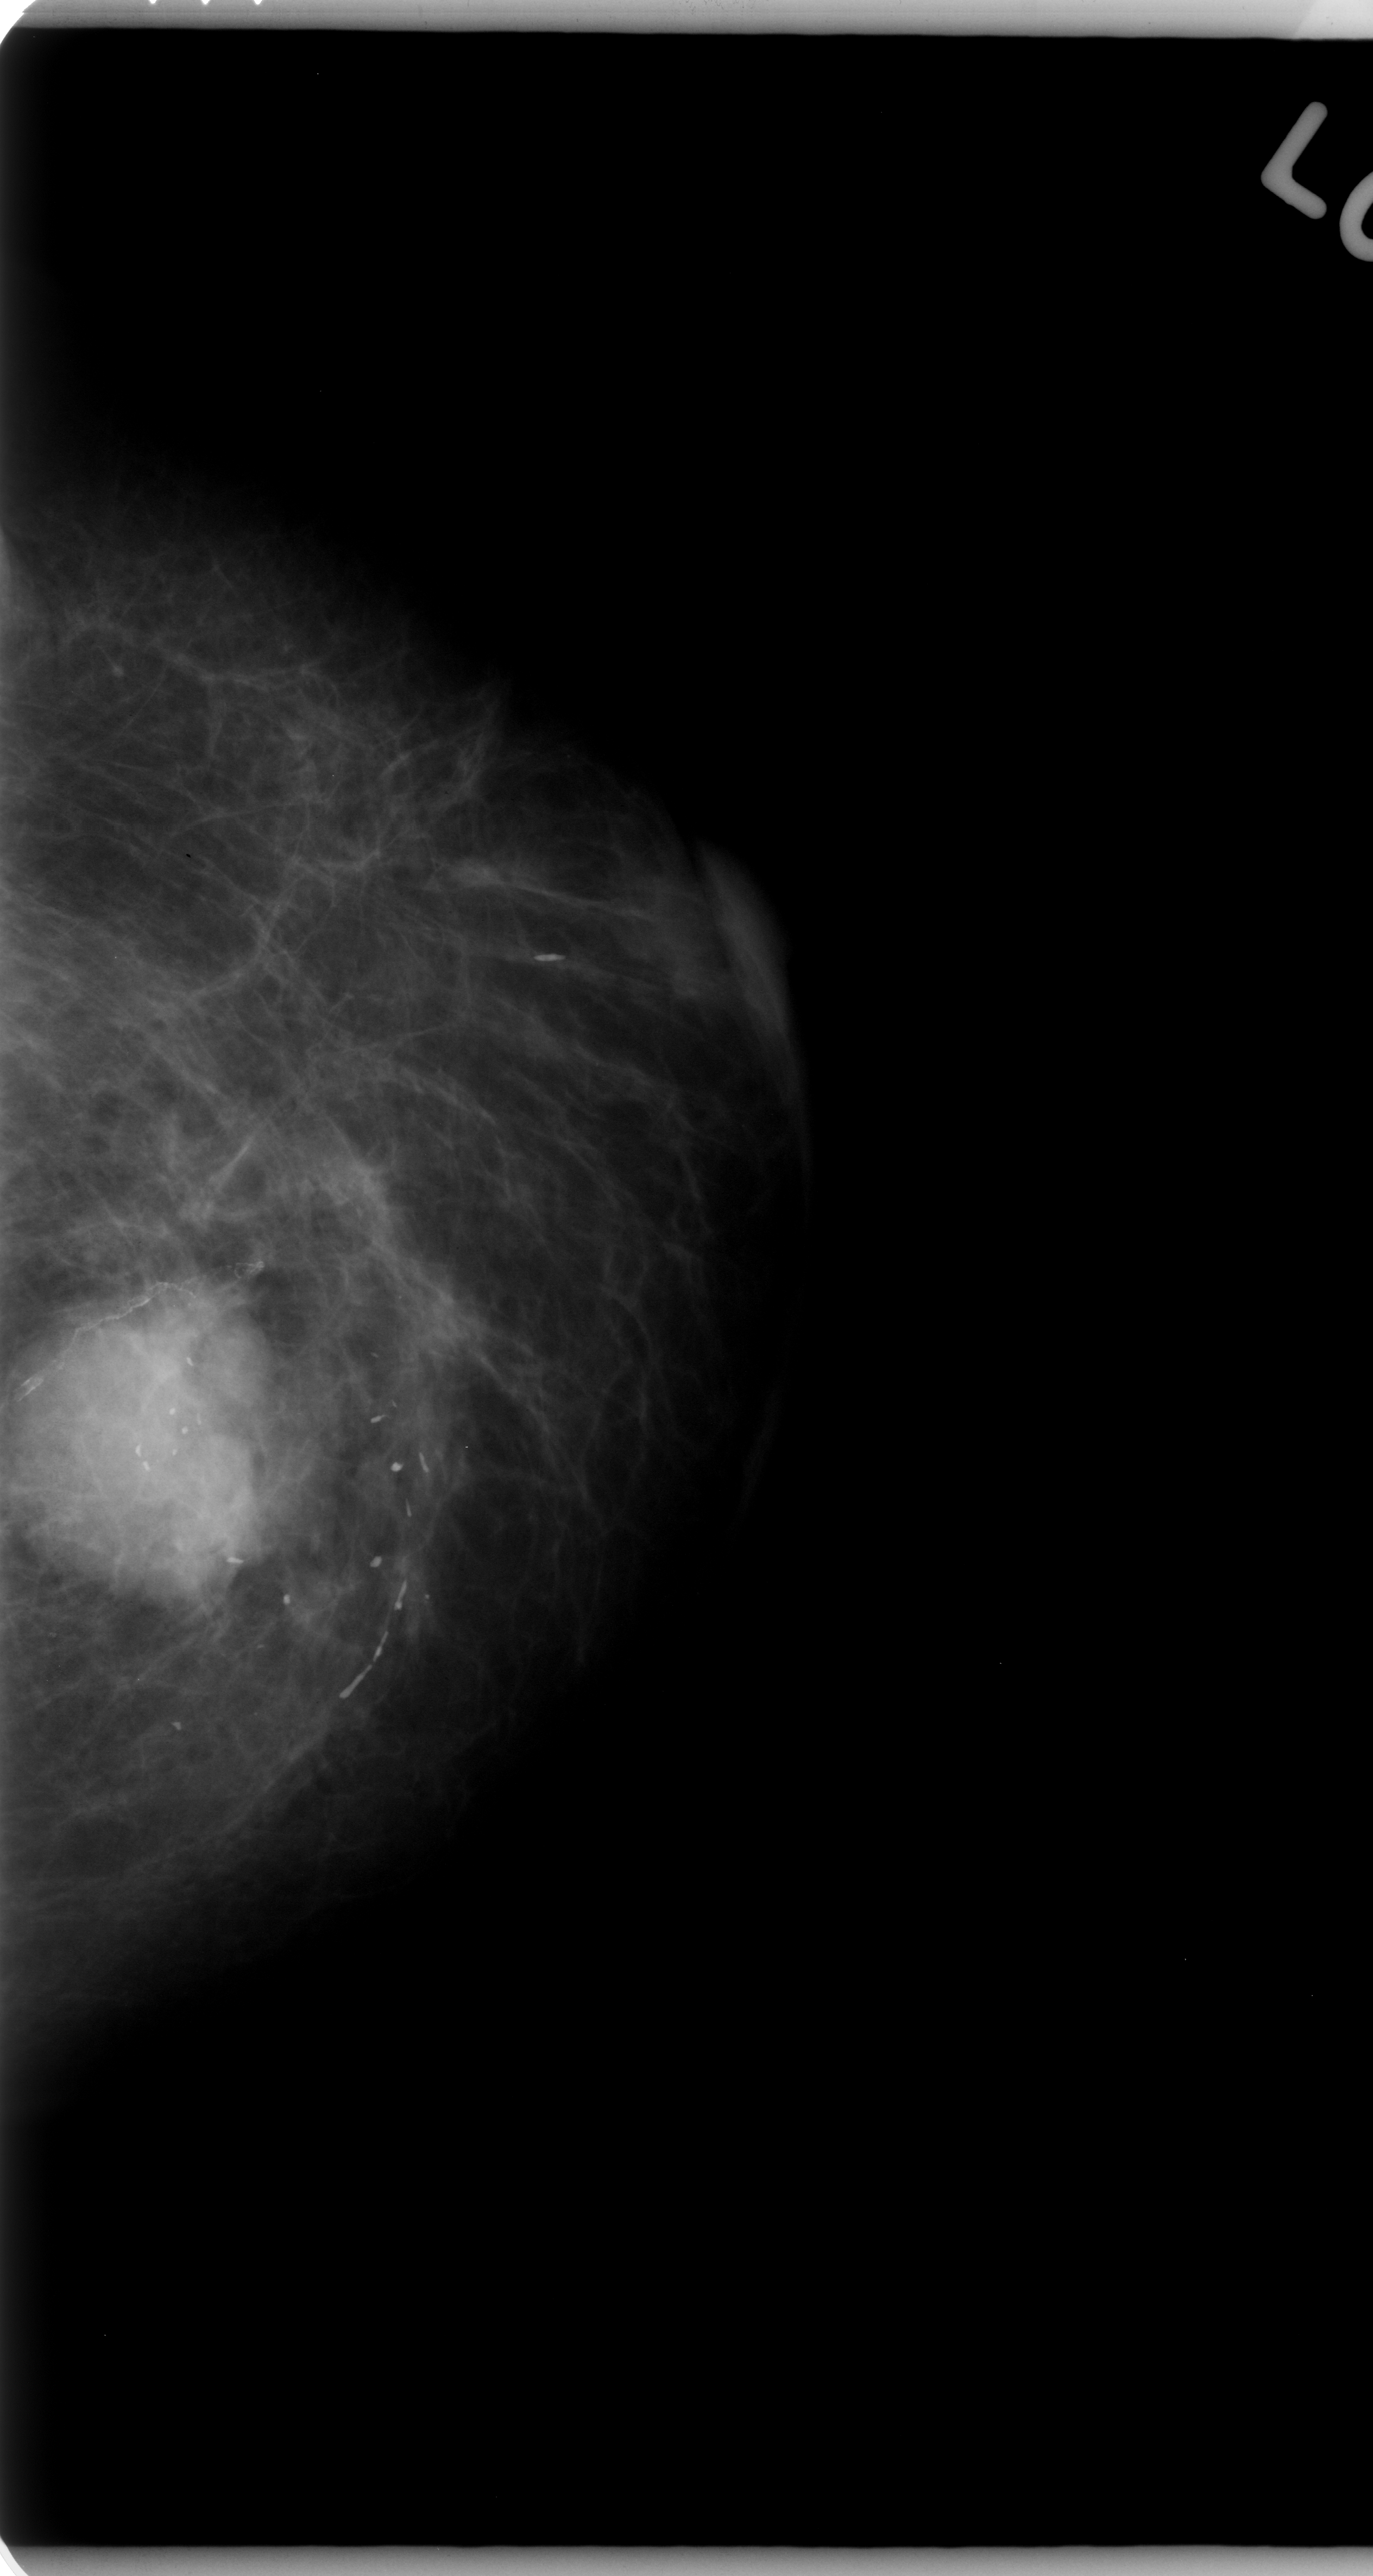
Digitized screen-film mammogram; left breast; CC view; 1373 × 2576 image matrix.
Marked abnormalities (boxes around the expert regions of interest):
- mass, shape lobulated, margins microlobulated; BI-RADS assessment category 5; subtlety rating 5 on a 1 (subtle) to 5 (obvious) scale; pathology (as recorded): malignant: bounding box <0,1265,257,1614> (left, top, right, bottom; pixels)